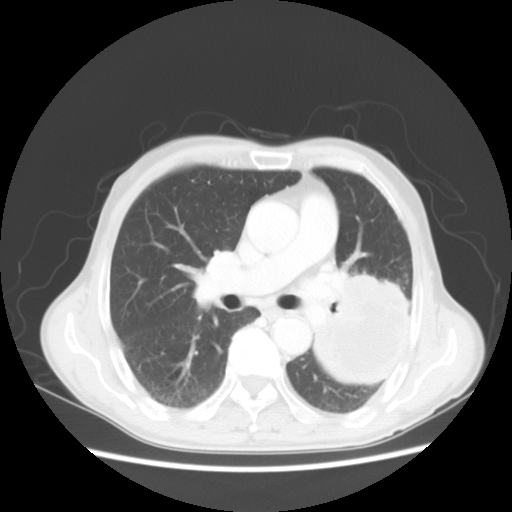
Chest CT, one axial slice. Slice 29 of 51 in the series (ordered by position). Reconstruction kernel STANDARD. 120 kVp. Lung window (W 1500 / L -600 HU). 5 mm slice thickness. 512 × 512 image matrix. Patient: male, 64 years. Case-level facts recorded for this patient, not image findings: clinical TNM (as recorded): T4 N0 M0.
Annotated regions visible in this slice (rectangle marked by the reading radiologist):
- lung tumour (recorded histology: squamous cell carcinoma): bounding box [x1, y1, x2, y2] px = [304, 260, 415, 392]